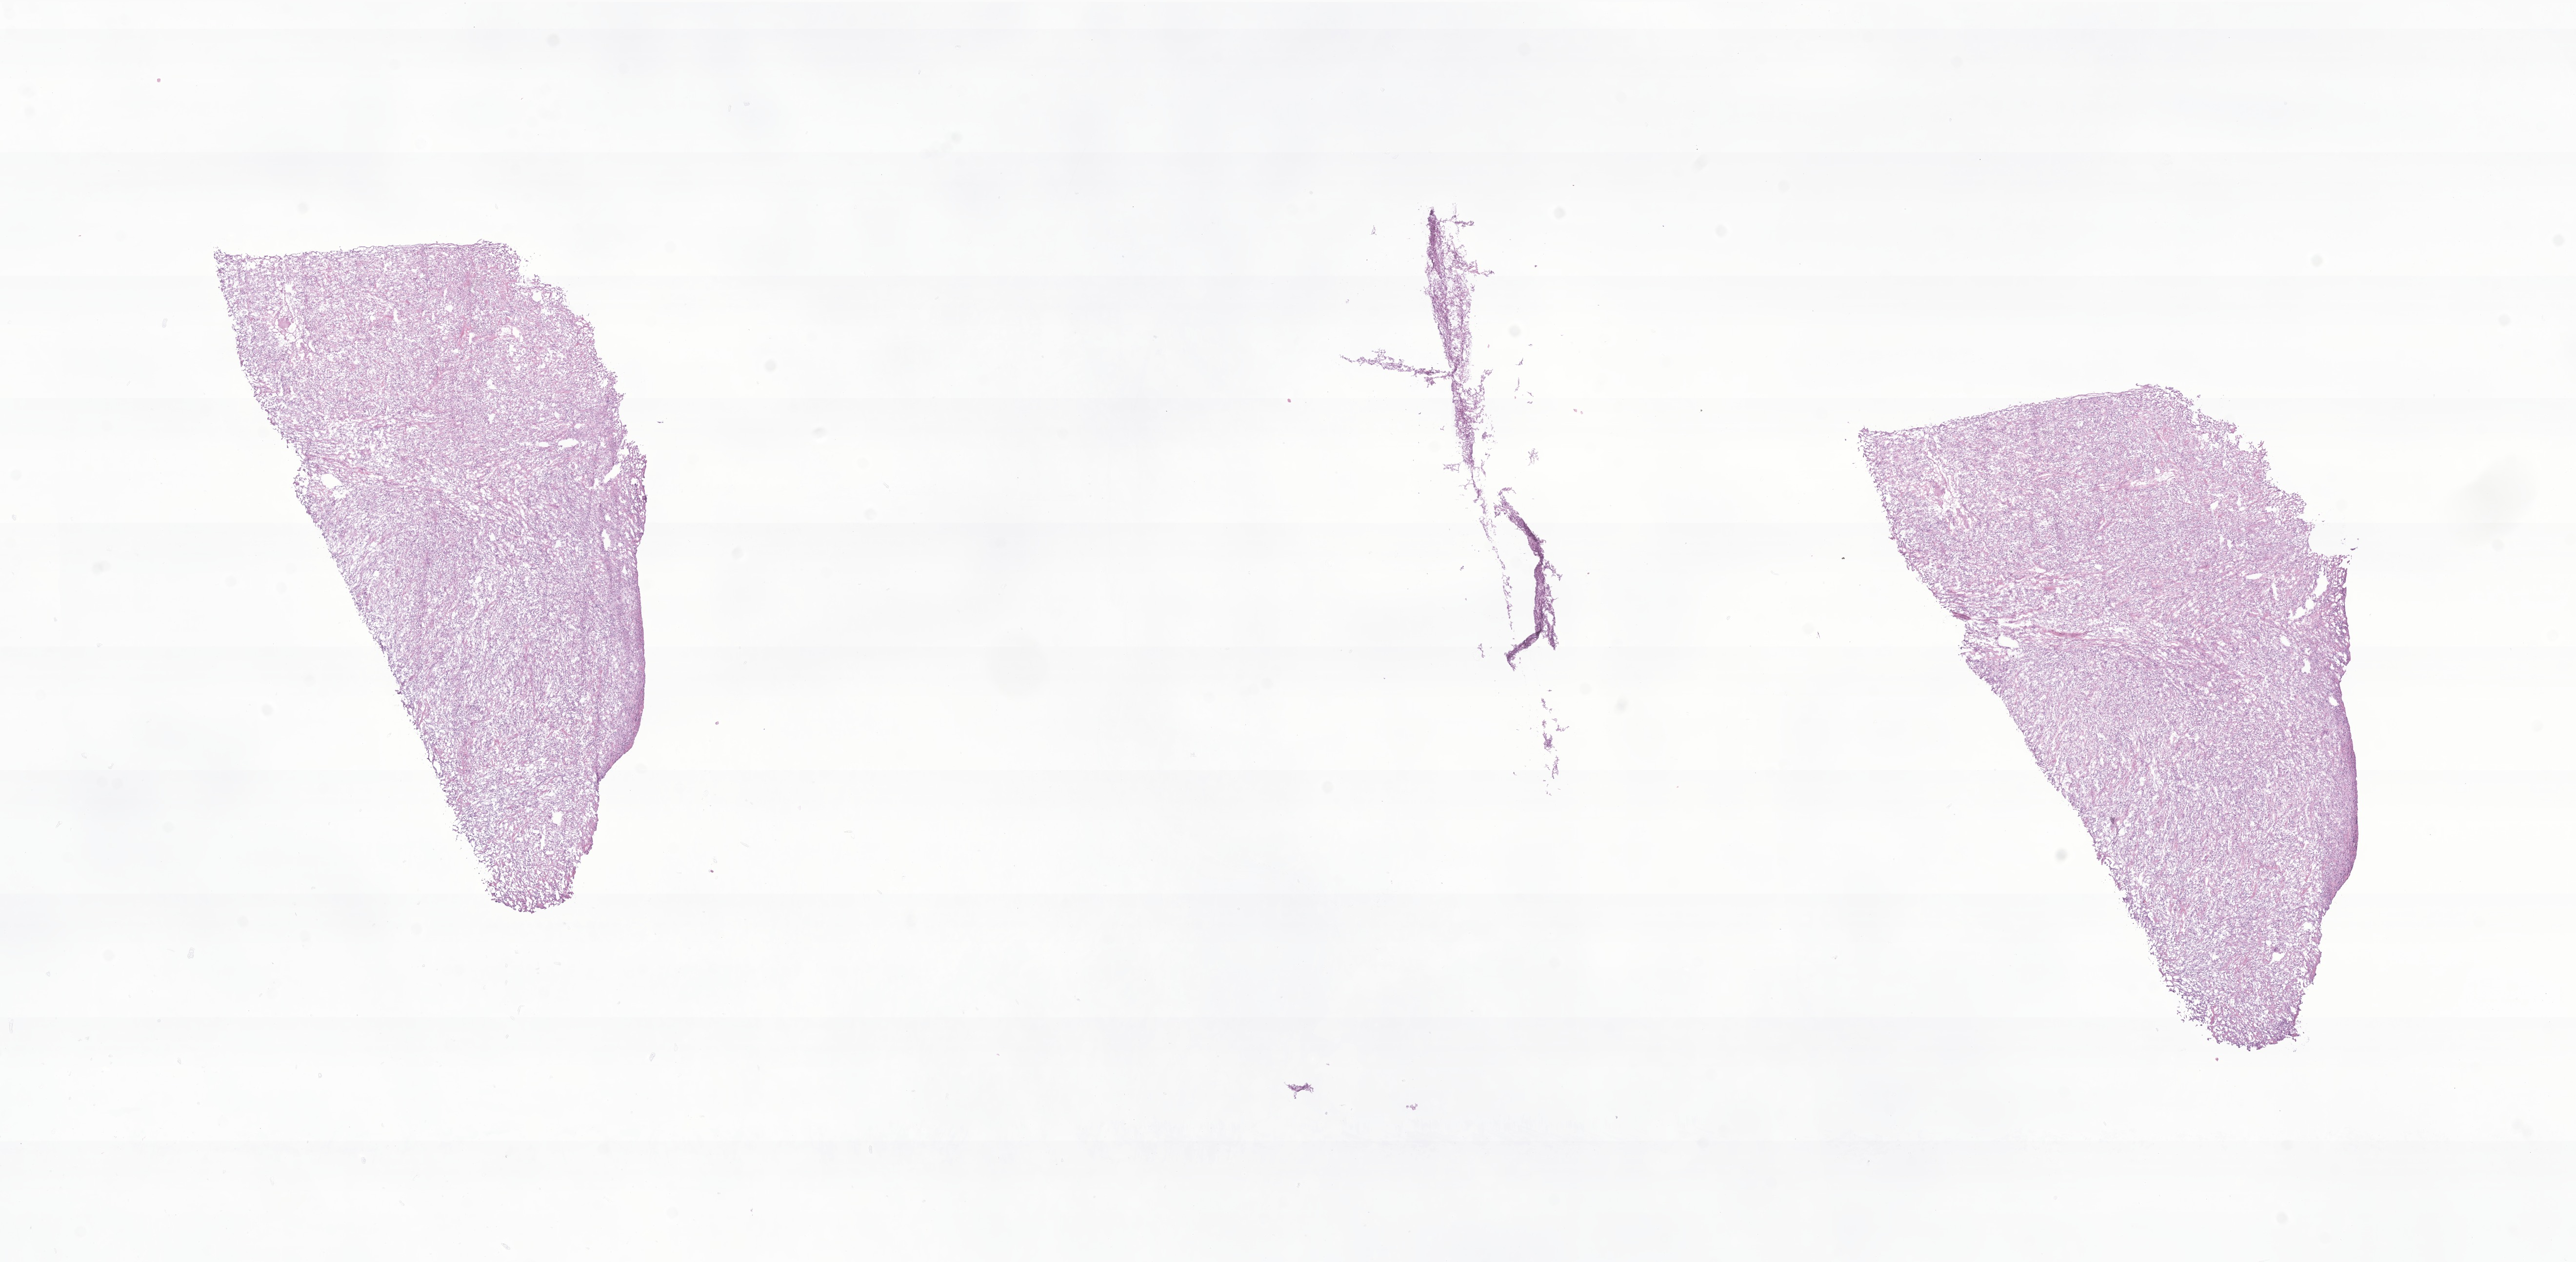
Digitized hematoxylin and eosin (H&E)-stained section of tumor tissue from the spinal cord, whole scanned area (about 22.3 x 10.9 mm) shown as a low-resolution overview, frozen section (OCT-embedded). Patient male; age 194 months.
Recorded diagnosis: Neoplasm, uncertain whether benign or malignant.